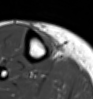
MRI of an extremity soft-tissue mass, one axial slice; position 14 of 54 along the scan axis; MR volume resampled by the dataset authors to the PET/CT grid (not the native acquisition matrix); 93 × 99 image matrix, field of view 91 × 97 mm. Female patient. Case-level facts recorded for this patient, not image findings: histological type: undifferentiated – high grade; grade: high; site of the primary tumour: right thigh.
Outlined on this slice (expert contour drawn on MRI and transferred to this co-registered scan by the dataset authors):
- gross tumour volume (mass): bounding box <36,29,58,53> (left, top, right, bottom; pixels)